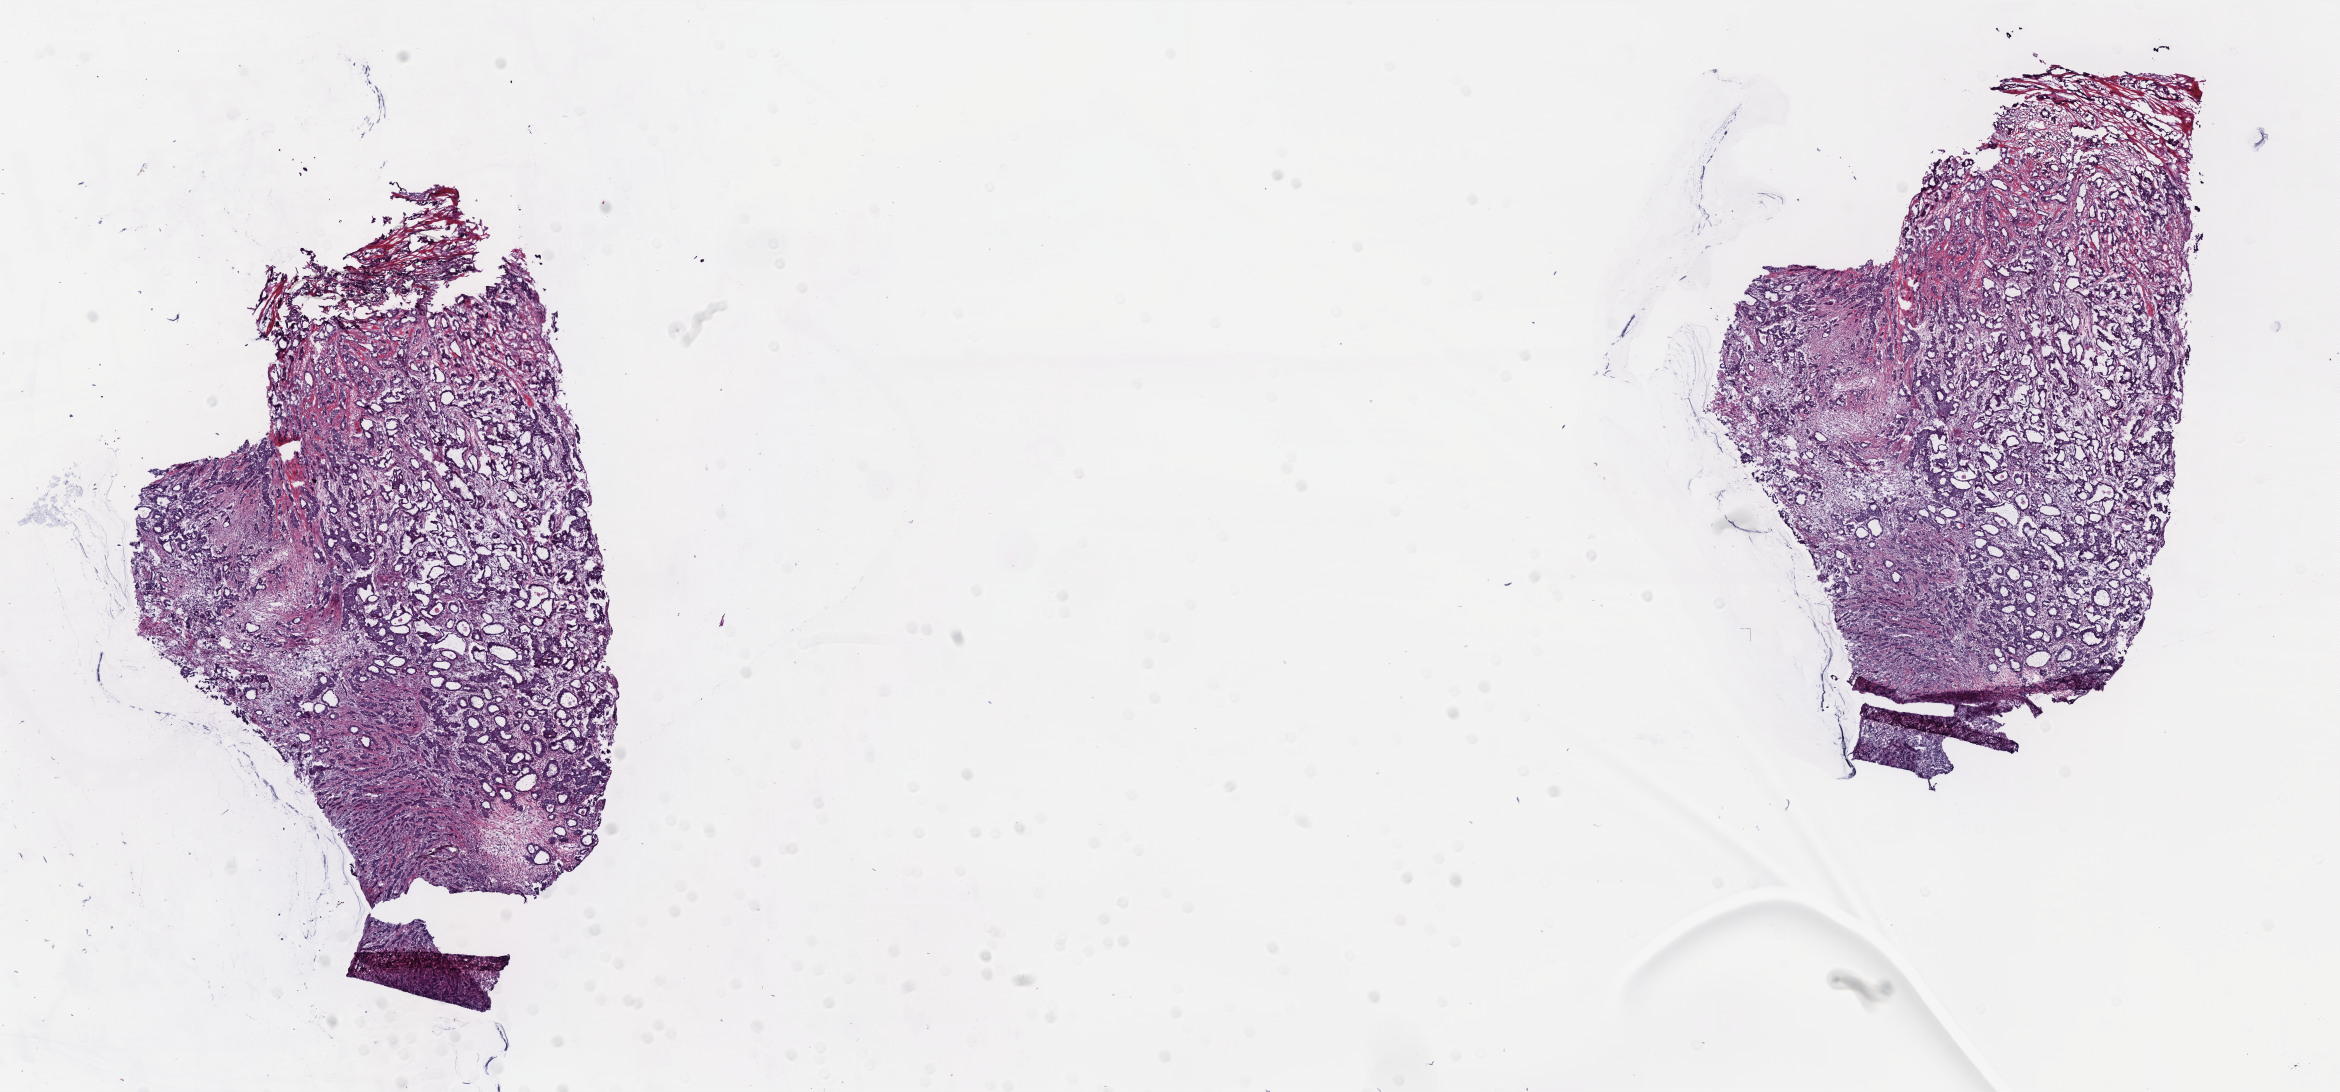
Whole-slide histology image, H&E, a low-resolution overview of the entire scanned area, about 18.8 x 8.8 mm (slide scanned at 40x); frozen section from the bottom of the tissue portion; primary tumour sample from the breast. Female patient; age at initial diagnosis 79 years. Composition of this section per pathologist review: tumour cells 75%, tumour nuclei 80%, normal cells 0%, stromal cells 23%, necrosis 2%. Infiltration values recorded for this section: lymphocyte infiltration 6%, monocyte infiltration 0%, neutrophil infiltration 0%.
- laterality: left
- histologic diagnosis: Infiltrating duct carcinoma, NOS
- AJCC pathologic stage: IIA